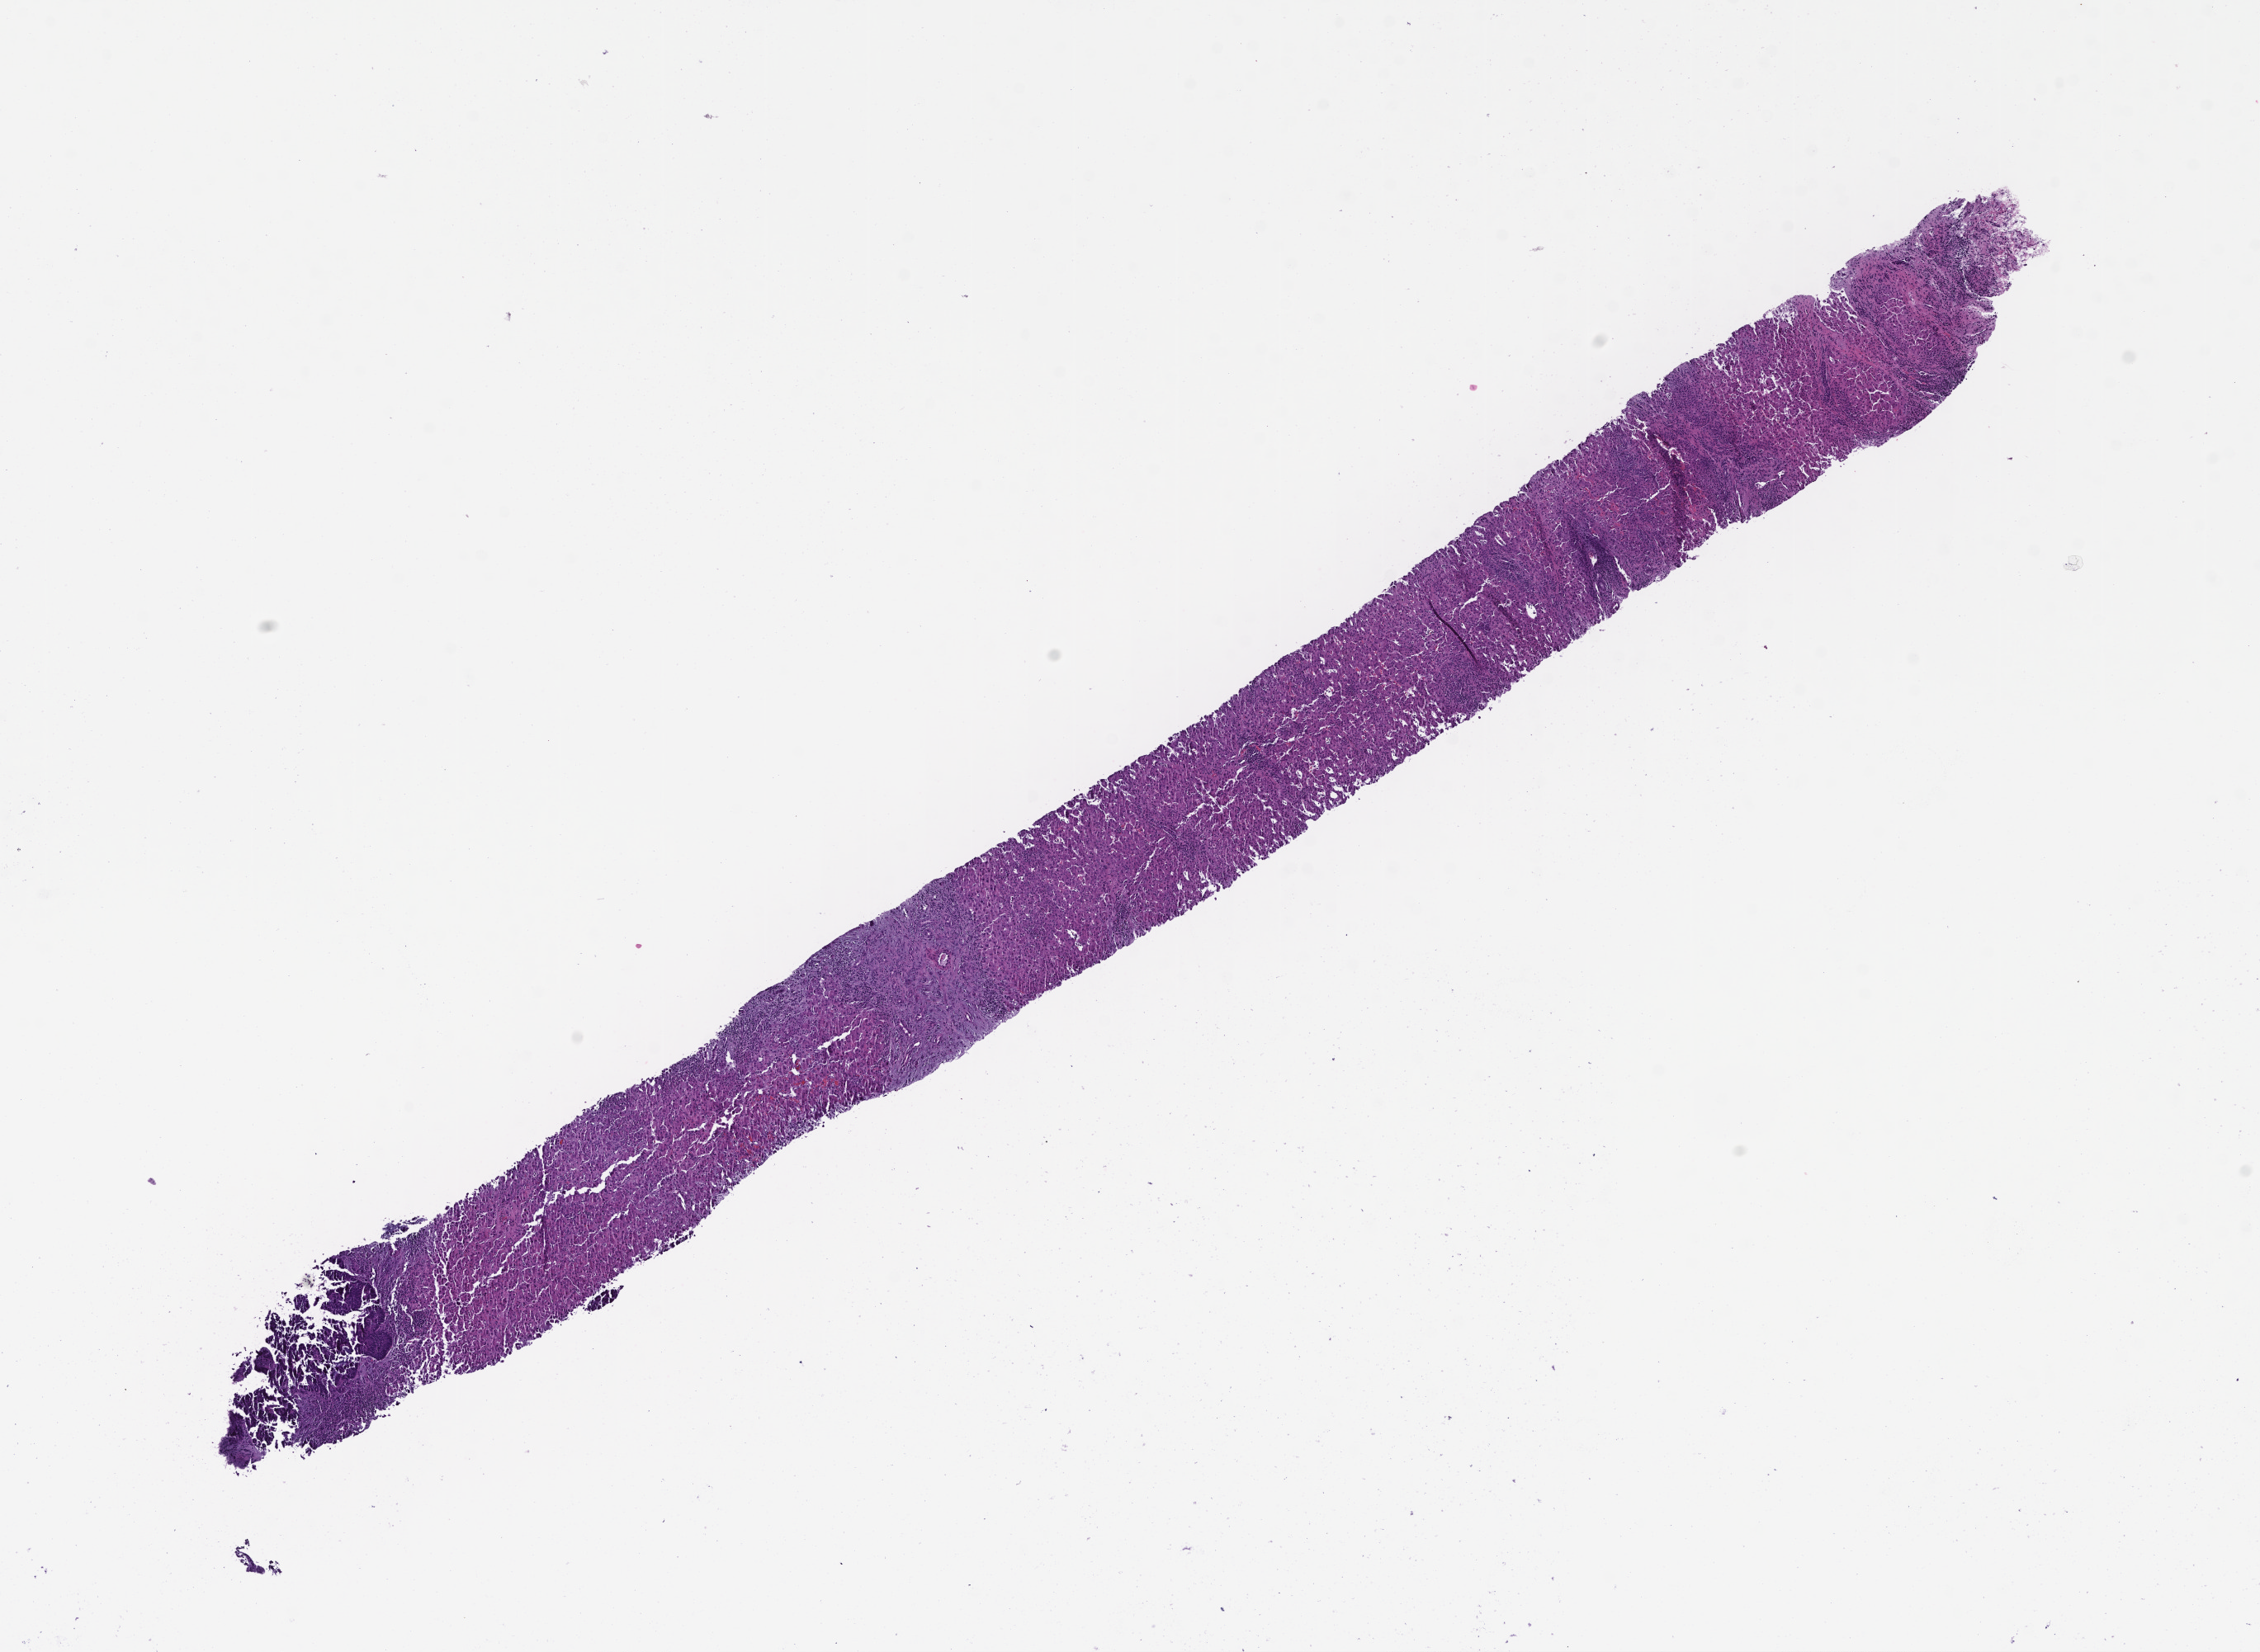
Haematoxylin and eosin whole-slide image, a low-resolution overview of the entire scanned area, about 11.1 x 8.1 mm; FFPE section; specimen time point: archival tissue. Patient sex: male.
This section: metastasis (sampled organ not recorded). Primary diagnosis of the patient: Colorectal Carcinoma.